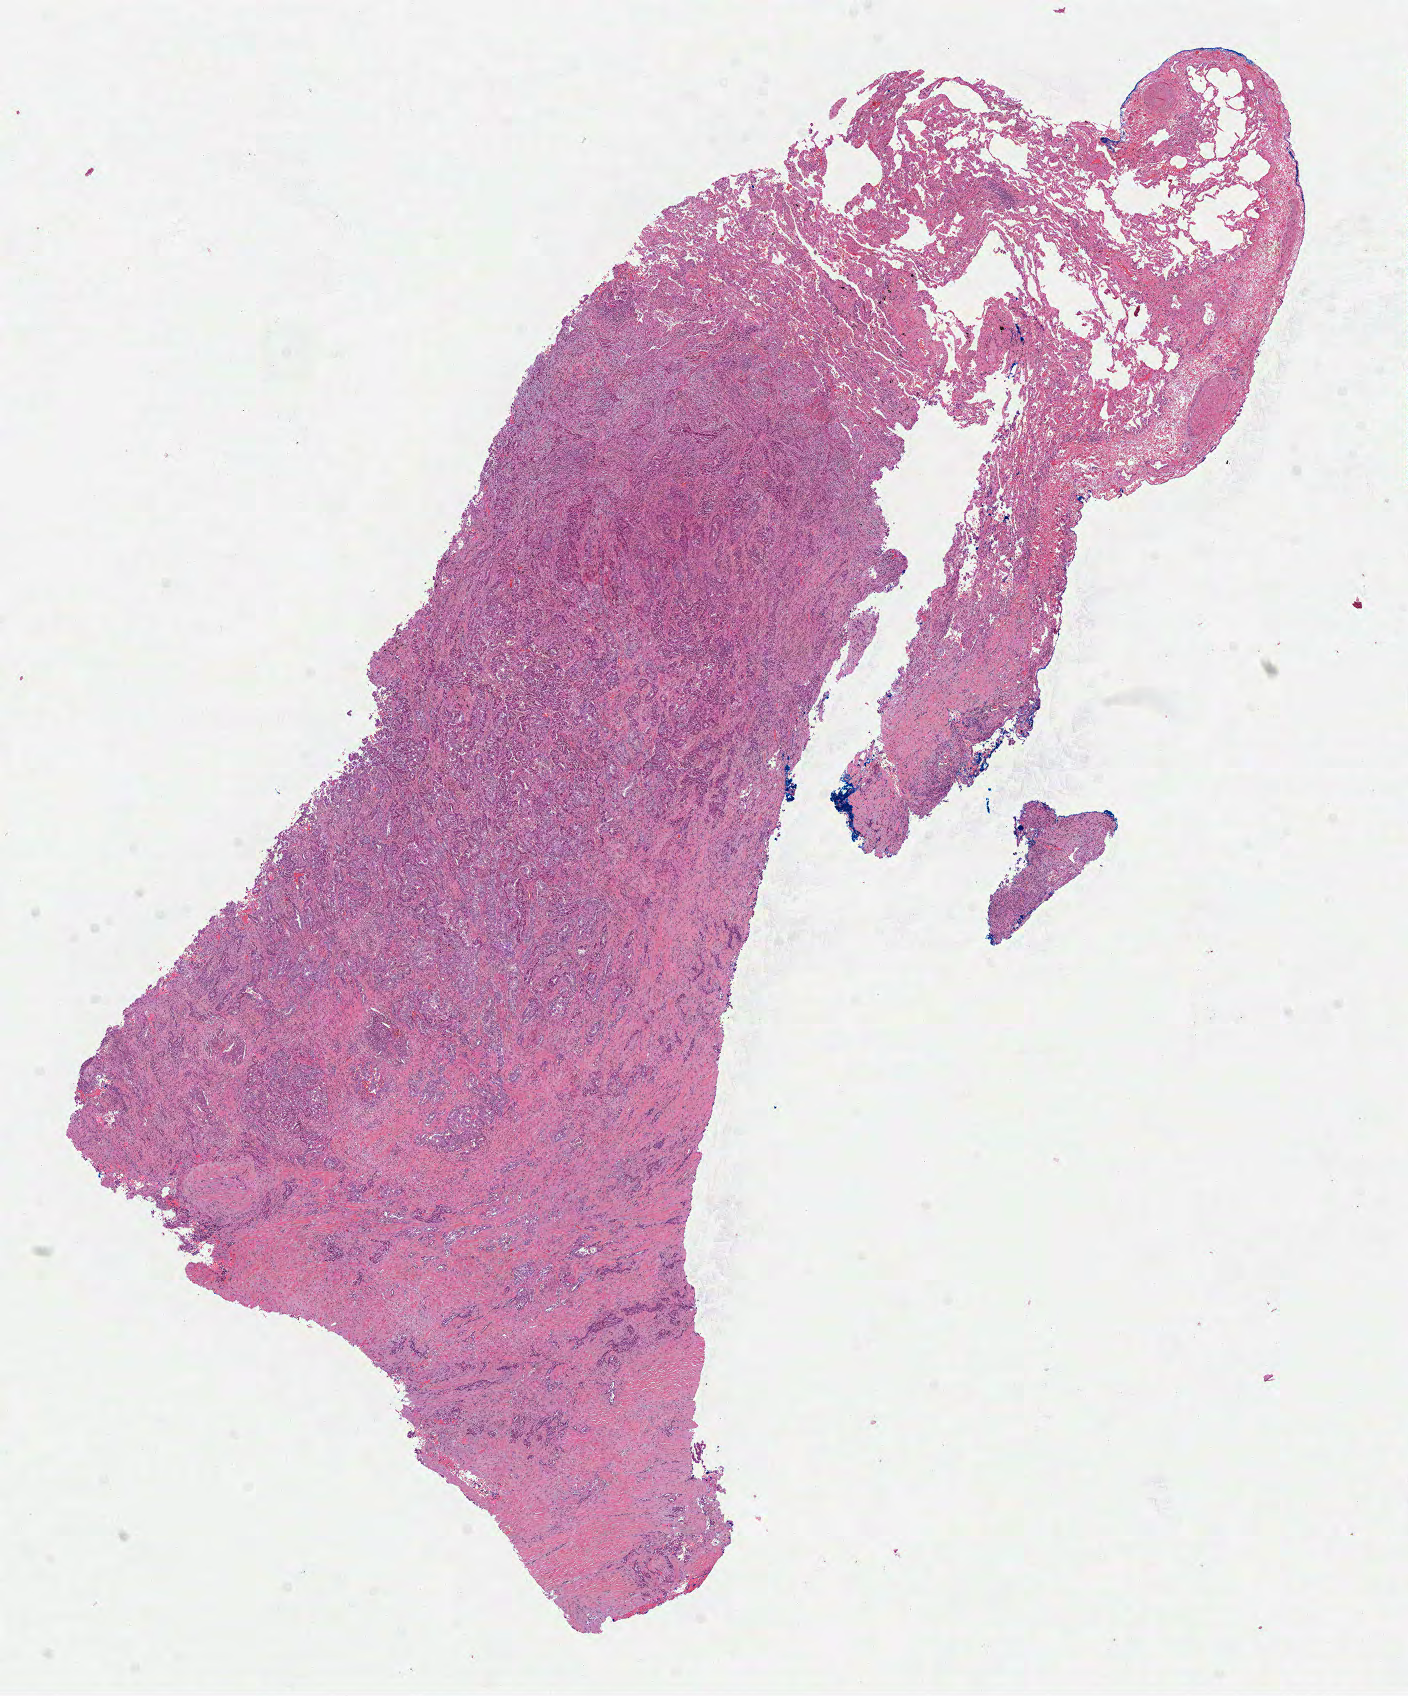
Whole-slide histology image, H&E-stained, low-resolution overview of the scanned area, about 11.4 x 13.7 mm (slide scanned at 40x); FFPE section; lung, primary tumour sample. Patient: female, age at initial diagnosis 64 years.
Diagnosis: Adenocarcinoma, NOS. AJCC pathologic stage: IB.